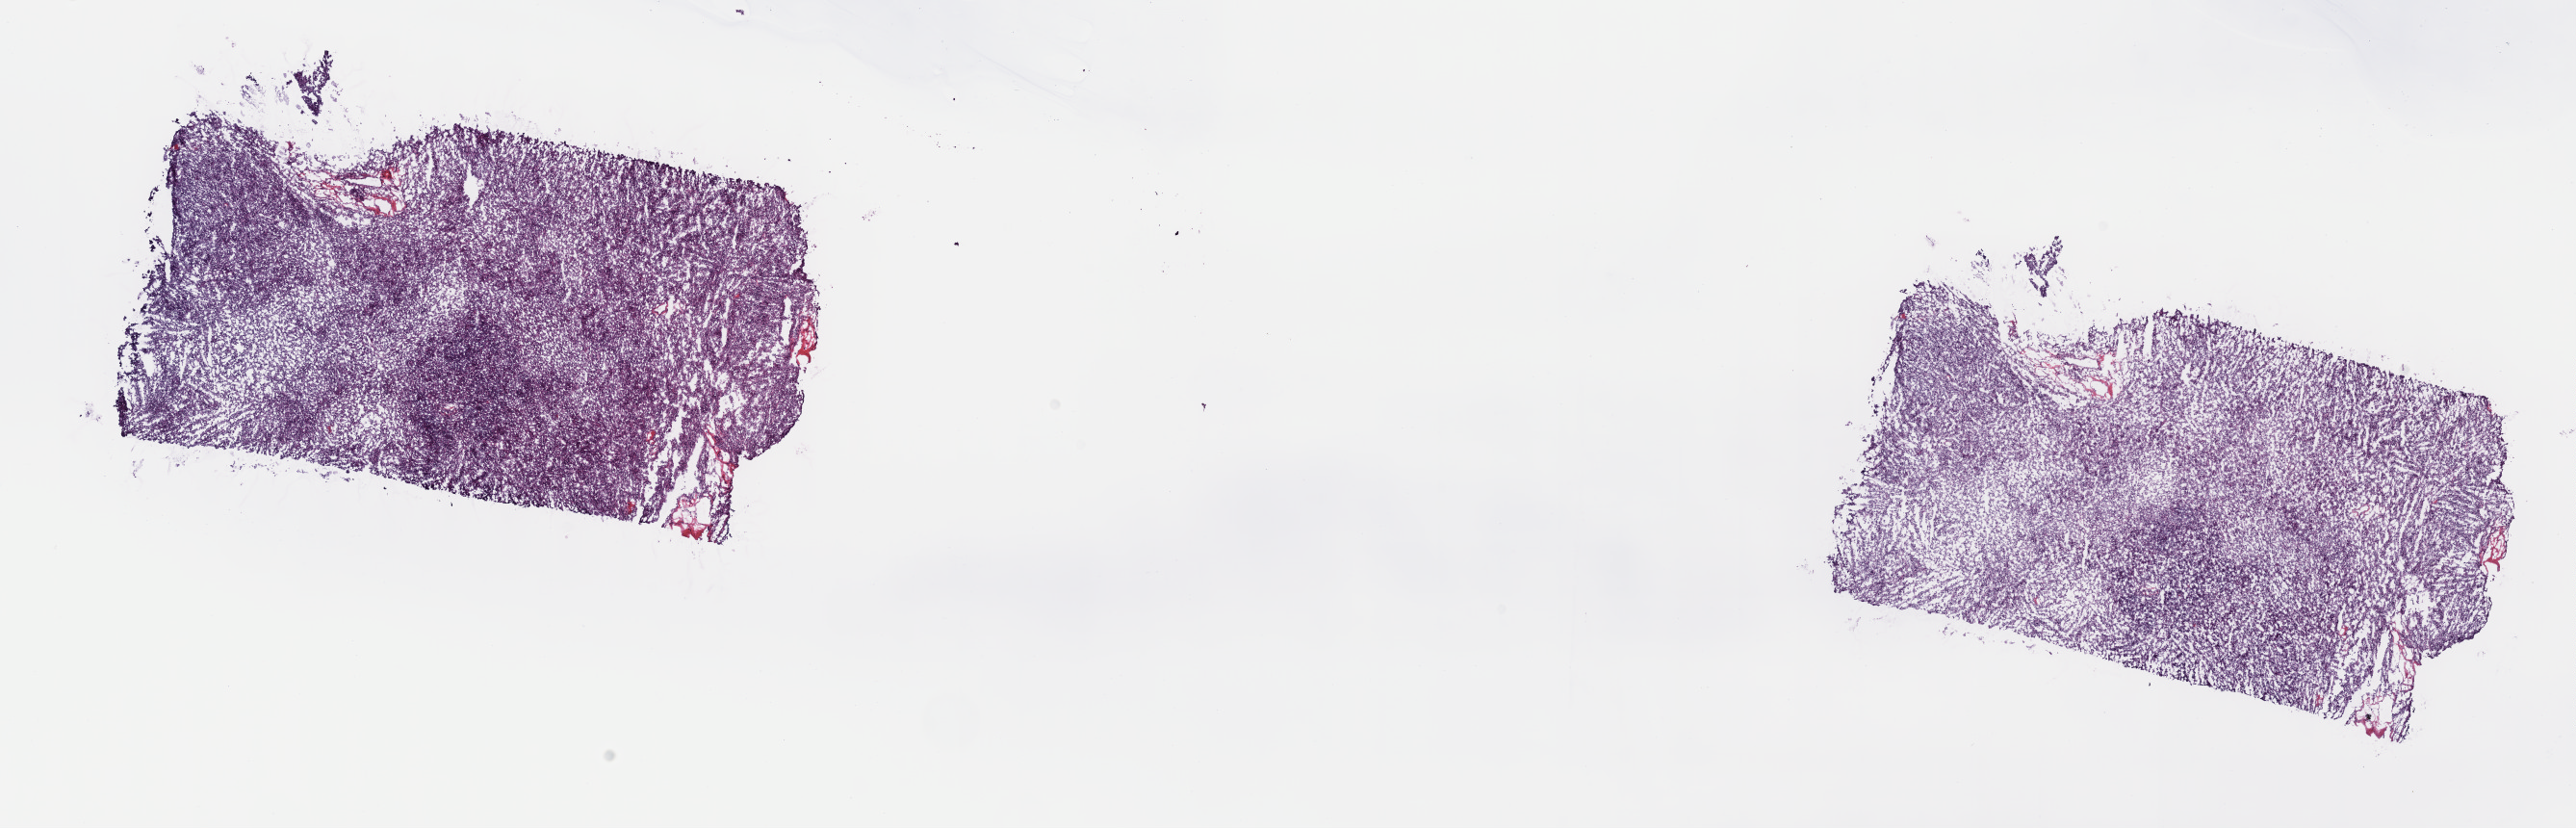
Whole-slide histology image, H&E-stained — whole scanned area (about 21.6 x 7.0 mm) shown as a low-resolution overview, frozen section from the top of the tissue portion, sample: primary tumour, thymus. Patient: female, age at initial diagnosis 50 years. Slide review estimates, as recorded: tumour cells 100%, tumour nuclei 80%, normal cells 0%, stromal cells 0%, necrosis 0%. Infiltration values recorded for this section: lymphocyte infiltration 2%, monocyte infiltration 0%, neutrophil infiltration 0%.
Diagnosis: Thymoma, type AB, NOS (anterior mediastinum).